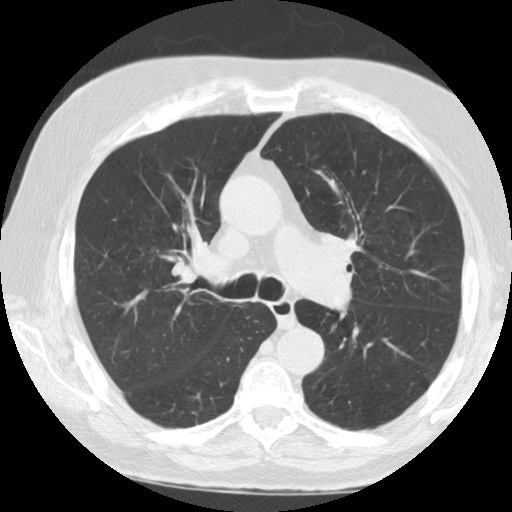
Chest CT (low-dose screening protocol), one axial image, second screening round (one year after baseline), lung window (W 1500 / L -600 HU), 2.5 mm slice thickness, 120 kVp, slice 44 of 110 in the series, 512 × 512 image matrix. Male, age 72 years at enrolment. Former smoker at enrolment.
Expert reader's lesion annotation, bounding box [x1, y1, x2, y2] px = [162, 225, 230, 296]. Screening reader's record for this exam: no non-calcified nodule ≥4 mm recorded. Official screen result: negative screen, minor abnormalities not suspicious for lung cancer. Later outcome: lung cancer diagnosed 415 days after this screen — small cell carcinoma, NOS, right upper lobe, stage IV (AJCC 6th edition), 7 mm at pathology.